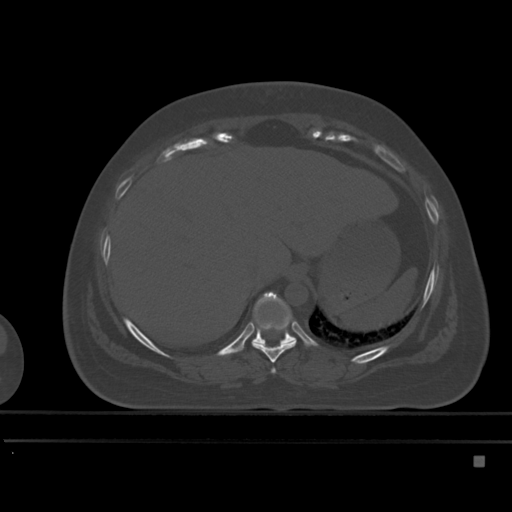
CT including the spine, one axial slice. Position 257 of 495 along the scan axis. Bone window (W 1800 / L 400 HU). 1.5 mm slice thickness. 512 × 512 image matrix, field of view 404 × 404 mm. Female patient, age 33 years. From the clinical record (not read from this slice): primary cancer: breast.
Structures marked on this image (semi-automatic segmentation, software-assisted and operator-edited):
- T10 vertebra: bounding box <252,293,296,344> (left, top, right, bottom; pixels)
- T8 vertebra: <271,368,276,374>
- T9 vertebra: <252,322,297,363>